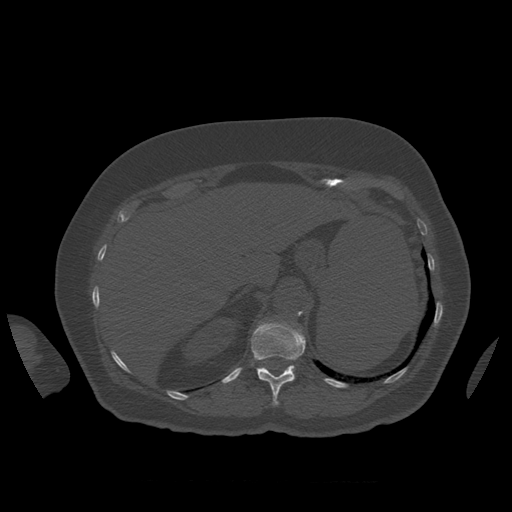
CT including the spine, one axial slice; slice 298 of 399 in the series (ordered by position); reconstruction kernel STANDARD; bone window (W 1800 / L 400 HU); 1.25 mm slice thickness; 512 × 512 image matrix, field of view 404 × 404 mm. Patient age 81 years. From the clinical record (not read from this slice): primary cancer: renal; vertebrae with lytic lesions (as recorded): L1.
Outlined on this slice (semi-automatic segmentation, software-assisted and operator-edited):
- L1 vertebra: box from (x=293, y=366) to (x=296, y=374) px
- T12 vertebra: (x=251, y=320)–(x=306, y=406)